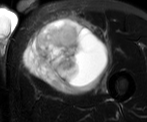
MRI of an extremity soft-tissue mass, one axial slice. Slice 39 of 52 in the series (ordered by position). T2-weighted fat-saturated. MR volume resampled by the dataset authors to the PET/CT grid (not the native acquisition matrix). 3.27 mm slice thickness. 147 × 122 image matrix, field of view 144 × 119 mm. Male patient. From the clinical record (not read from this slice): histological type: pleiomorphic liposarcoma; grade: high; site of the primary tumour: left thigh.
Outlined on this slice (expert contour drawn on MRI and transferred to this co-registered scan by the dataset authors):
- gross tumour volume including surrounding oedema: bounding box <25,16,110,90> (left, top, right, bottom; pixels)
- gross tumour volume (mass): <25,21,106,90>